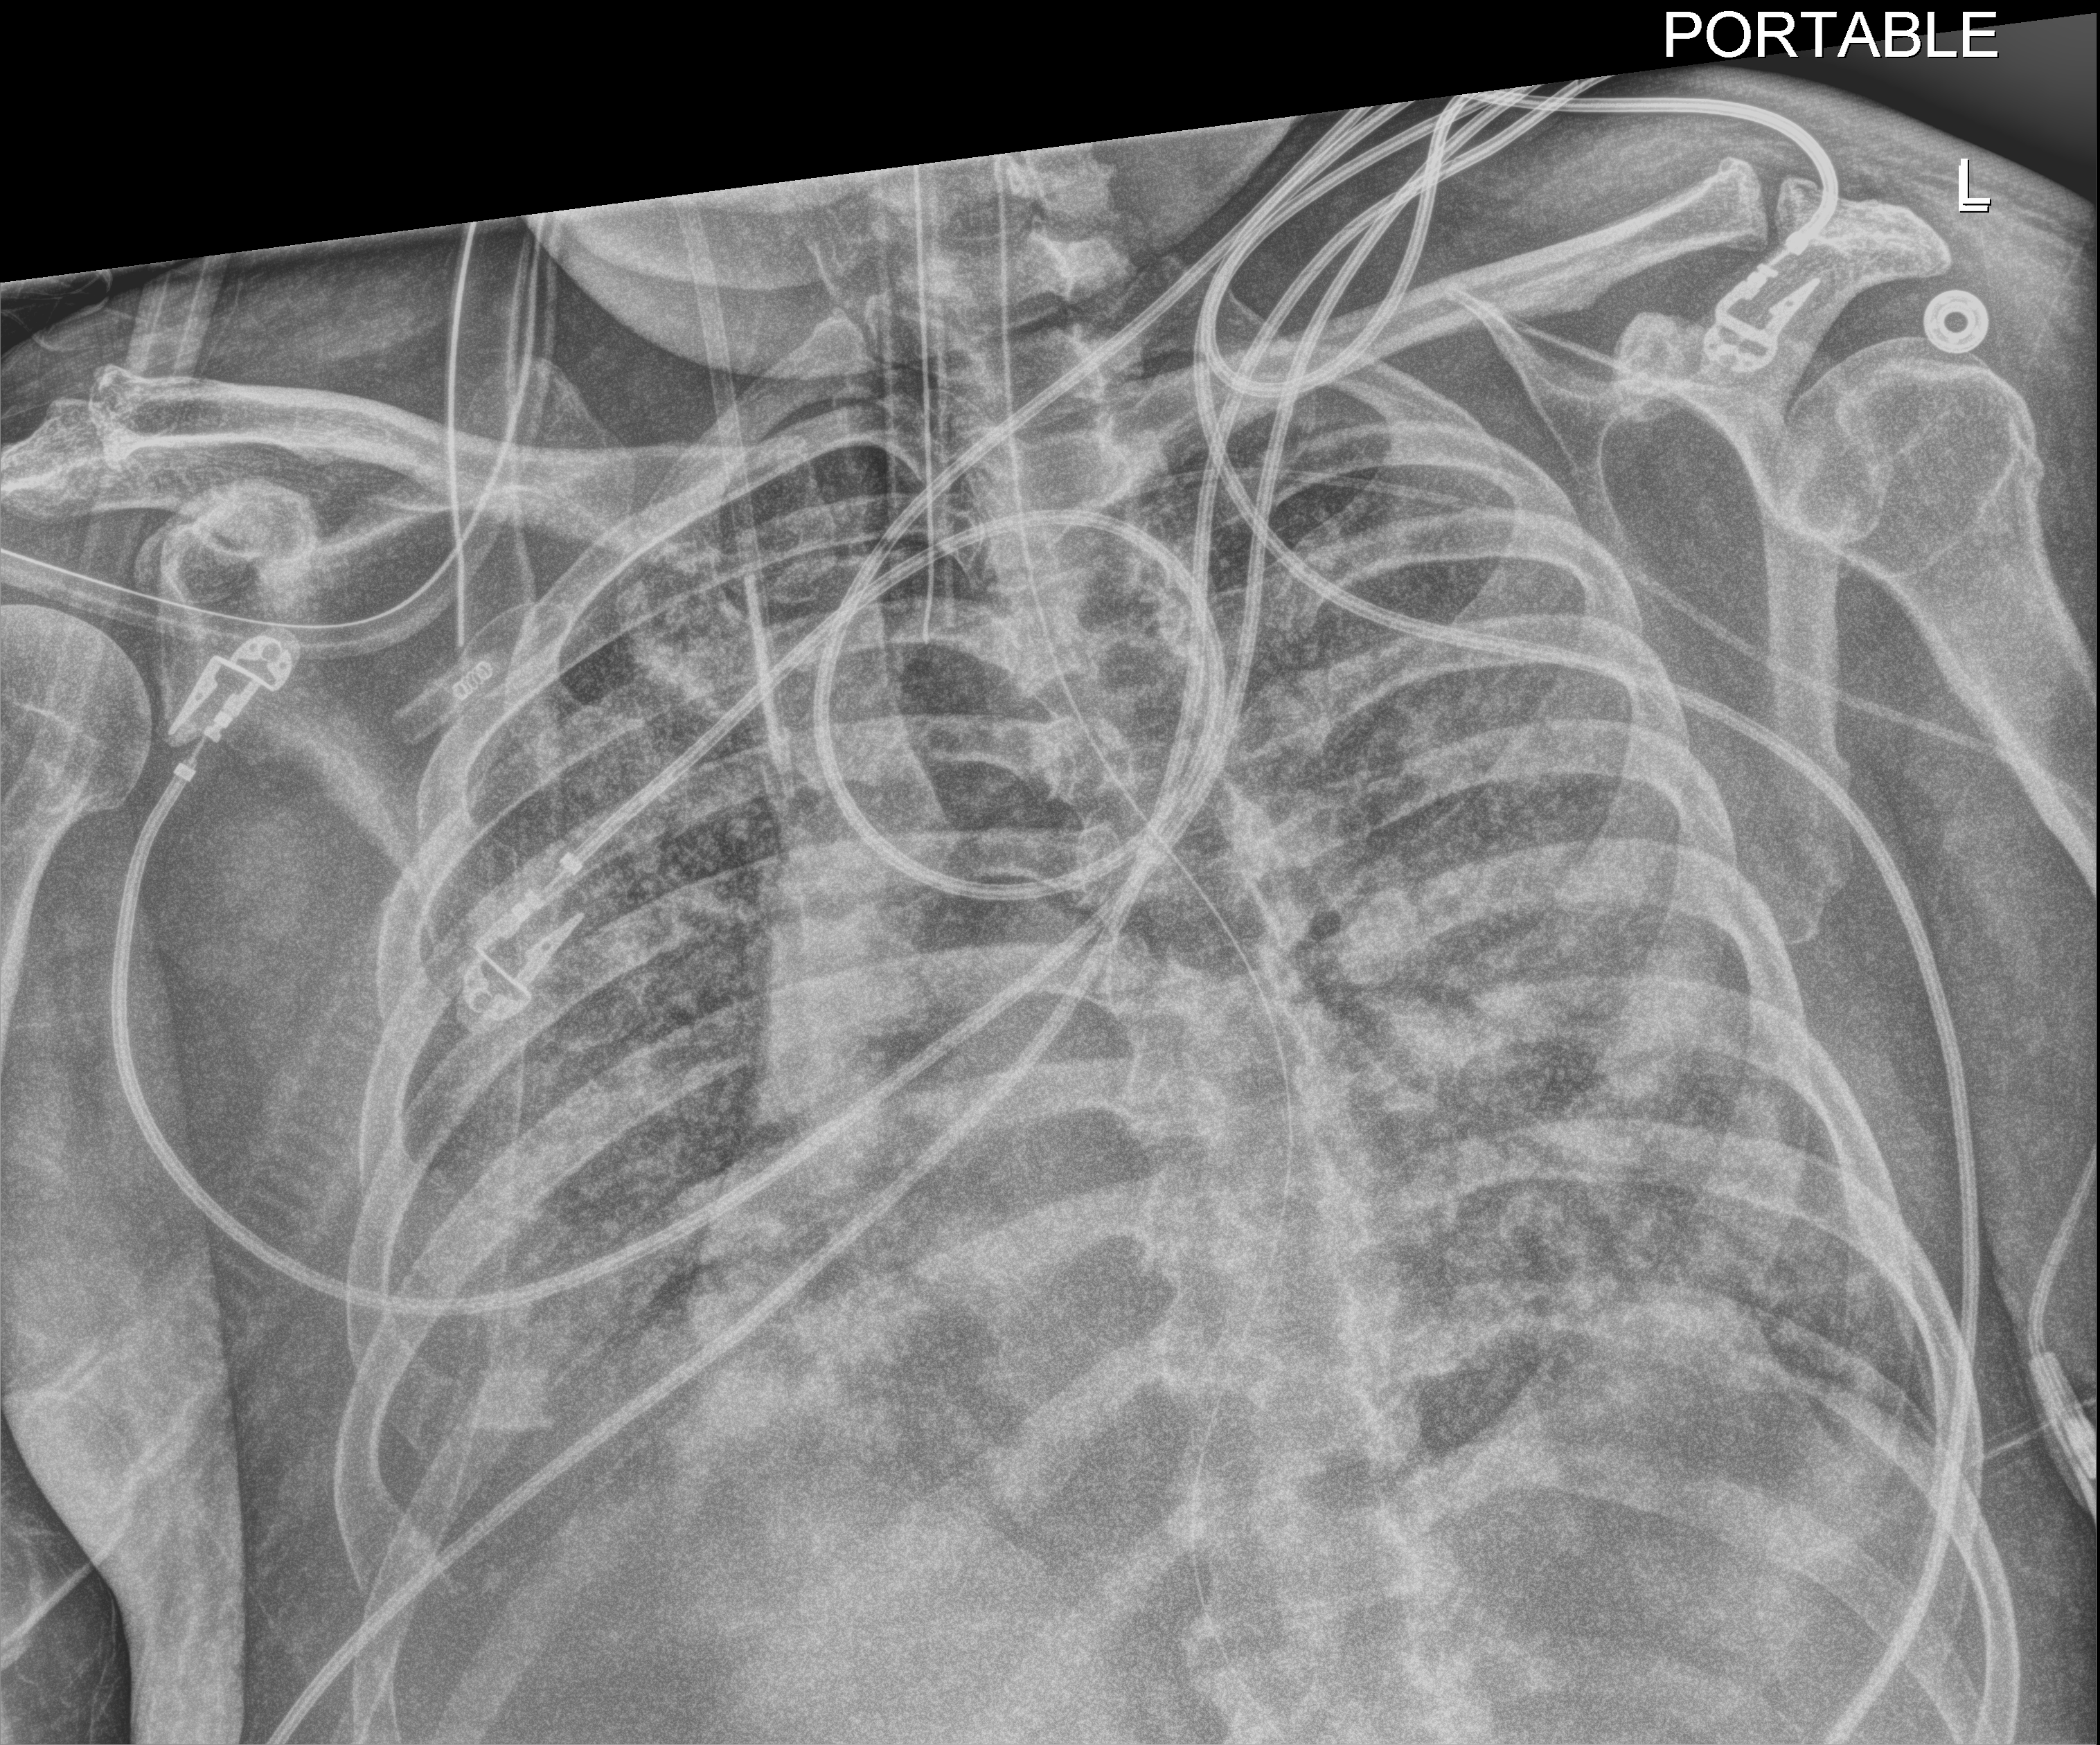
Chest X-ray (portable); anteroposterior (AP) projection. Patient hospitalised with COVID-19; male, aged 60–74 years.
From the hospital-stay record, not from the radiograph (when in the stay this image was taken is not recorded): diabetes (admission record): no; mechanically ventilated during this hospital stay: yes.